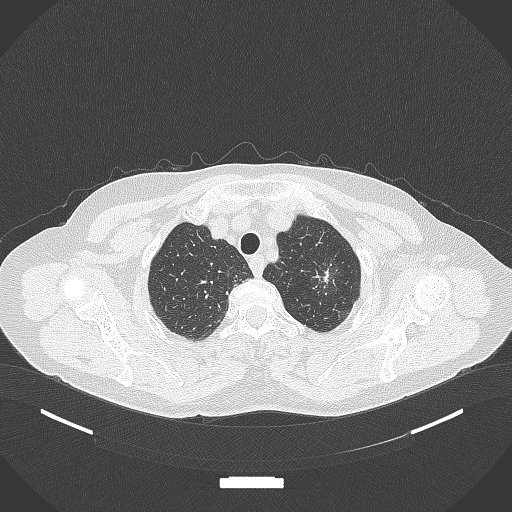
Chest CT, one axial slice. Position 313 of 369 along the scan axis. Reconstruction kernel B70f. Lung window (W 1500 / L -600 HU). 512 × 512 image matrix, field of view 400 × 400 mm. Patient: female, 64 years. From the clinical record (not read from this slice): clinical TNM (as recorded): T1c N0 M0; histopathological grade: G1.
Outlined on this slice (bounding box drawn by a radiologist):
- lung tumour (recorded histology: adenocarcinoma): box from (x=307, y=258) to (x=344, y=304) px